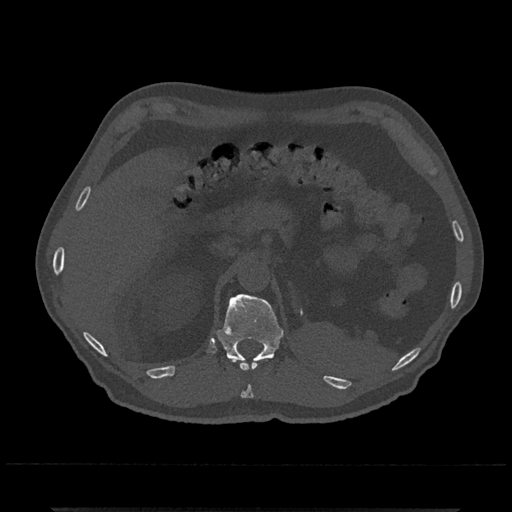
CT including the spine, one axial slice. Slice 448 of 797 in the series (ordered by position). Reconstruction kernel Br40s/3. 120 kVp. Bone window (W 1800 / L 400 HU). 0.5 mm slice thickness. 512 × 512 image matrix, field of view 393 × 393 mm. Patient: male, 67 years. Case-level facts recorded for this patient, not image findings: primary cancer: prostate.
Structures marked on this image (semi-automatically segmented with operator editing):
- T11 vertebra: bounding box <230,358,265,398> (left, top, right, bottom; pixels)
- T12 vertebra: <216,293,284,363>